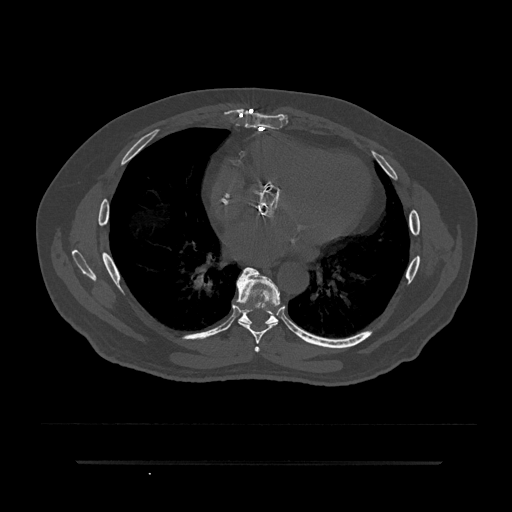
CT including the spine, one axial slice. Position 458 of 797 along the scan axis. 120 kVp. Bone window (W 1800 / L 400 HU). 0.5 mm slice thickness. 512 × 512 image matrix. Male patient, age 59 years. From the clinical record (not read from this slice): primary cancer: bile ducts.
Annotated regions visible in this slice (semi-automatically segmented with operator editing):
- T6 vertebra: bounding box <254,346,260,353> (left, top, right, bottom; pixels)
- T7 vertebra: <233,267,281,344>
- T8 vertebra: <223,308,297,335>